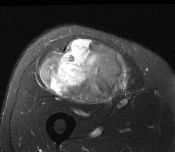
MRI of an extremity soft-tissue mass, one axial slice. Slice 84 of 116 in the series (ordered by position). T2-weighted fat-saturated. MR volume resampled by the dataset authors to the PET/CT grid (not the native acquisition matrix). 3.27 mm slice thickness. 175 × 152 image matrix. Male patient. From the clinical record (not read from this slice): histological type: pleiomorphic leiomyosarcoma; grade: intermediate; site of the primary tumour: right thigh.
Annotated regions visible in this slice (expert contour drawn on MRI and transferred to this co-registered scan by the dataset authors):
- gross tumour volume including surrounding oedema: bounding box (x1, y1, x2, y2) in pixels: (40, 38, 128, 105)
- gross tumour volume (mass): (40, 38, 128, 105)